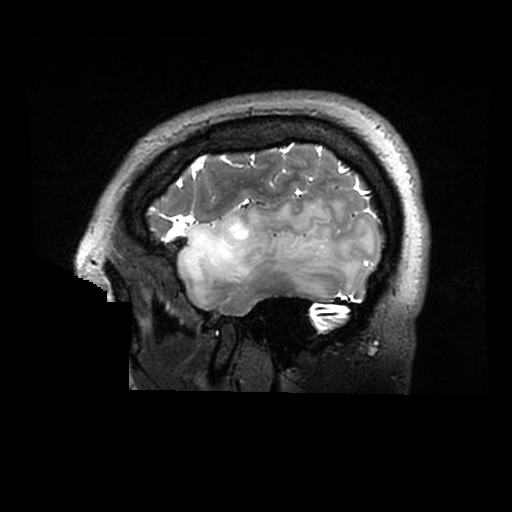
Brain MRI from a brain-tumour surgery series, one sagittal slice; position 240 of 320 along the scan axis; 0.6 mm slice thickness; 512 × 512 image matrix, field of view 240 × 240 mm. Case-level facts recorded for this patient, not image findings: histopathology: Astrocytoma; WHO grade: 2; IDH mutation: yes.
Outlined on this slice (expert manual segmentation):
- tumour: bounding box (x1, y1, x2, y2) in pixels: (178, 200, 367, 298)